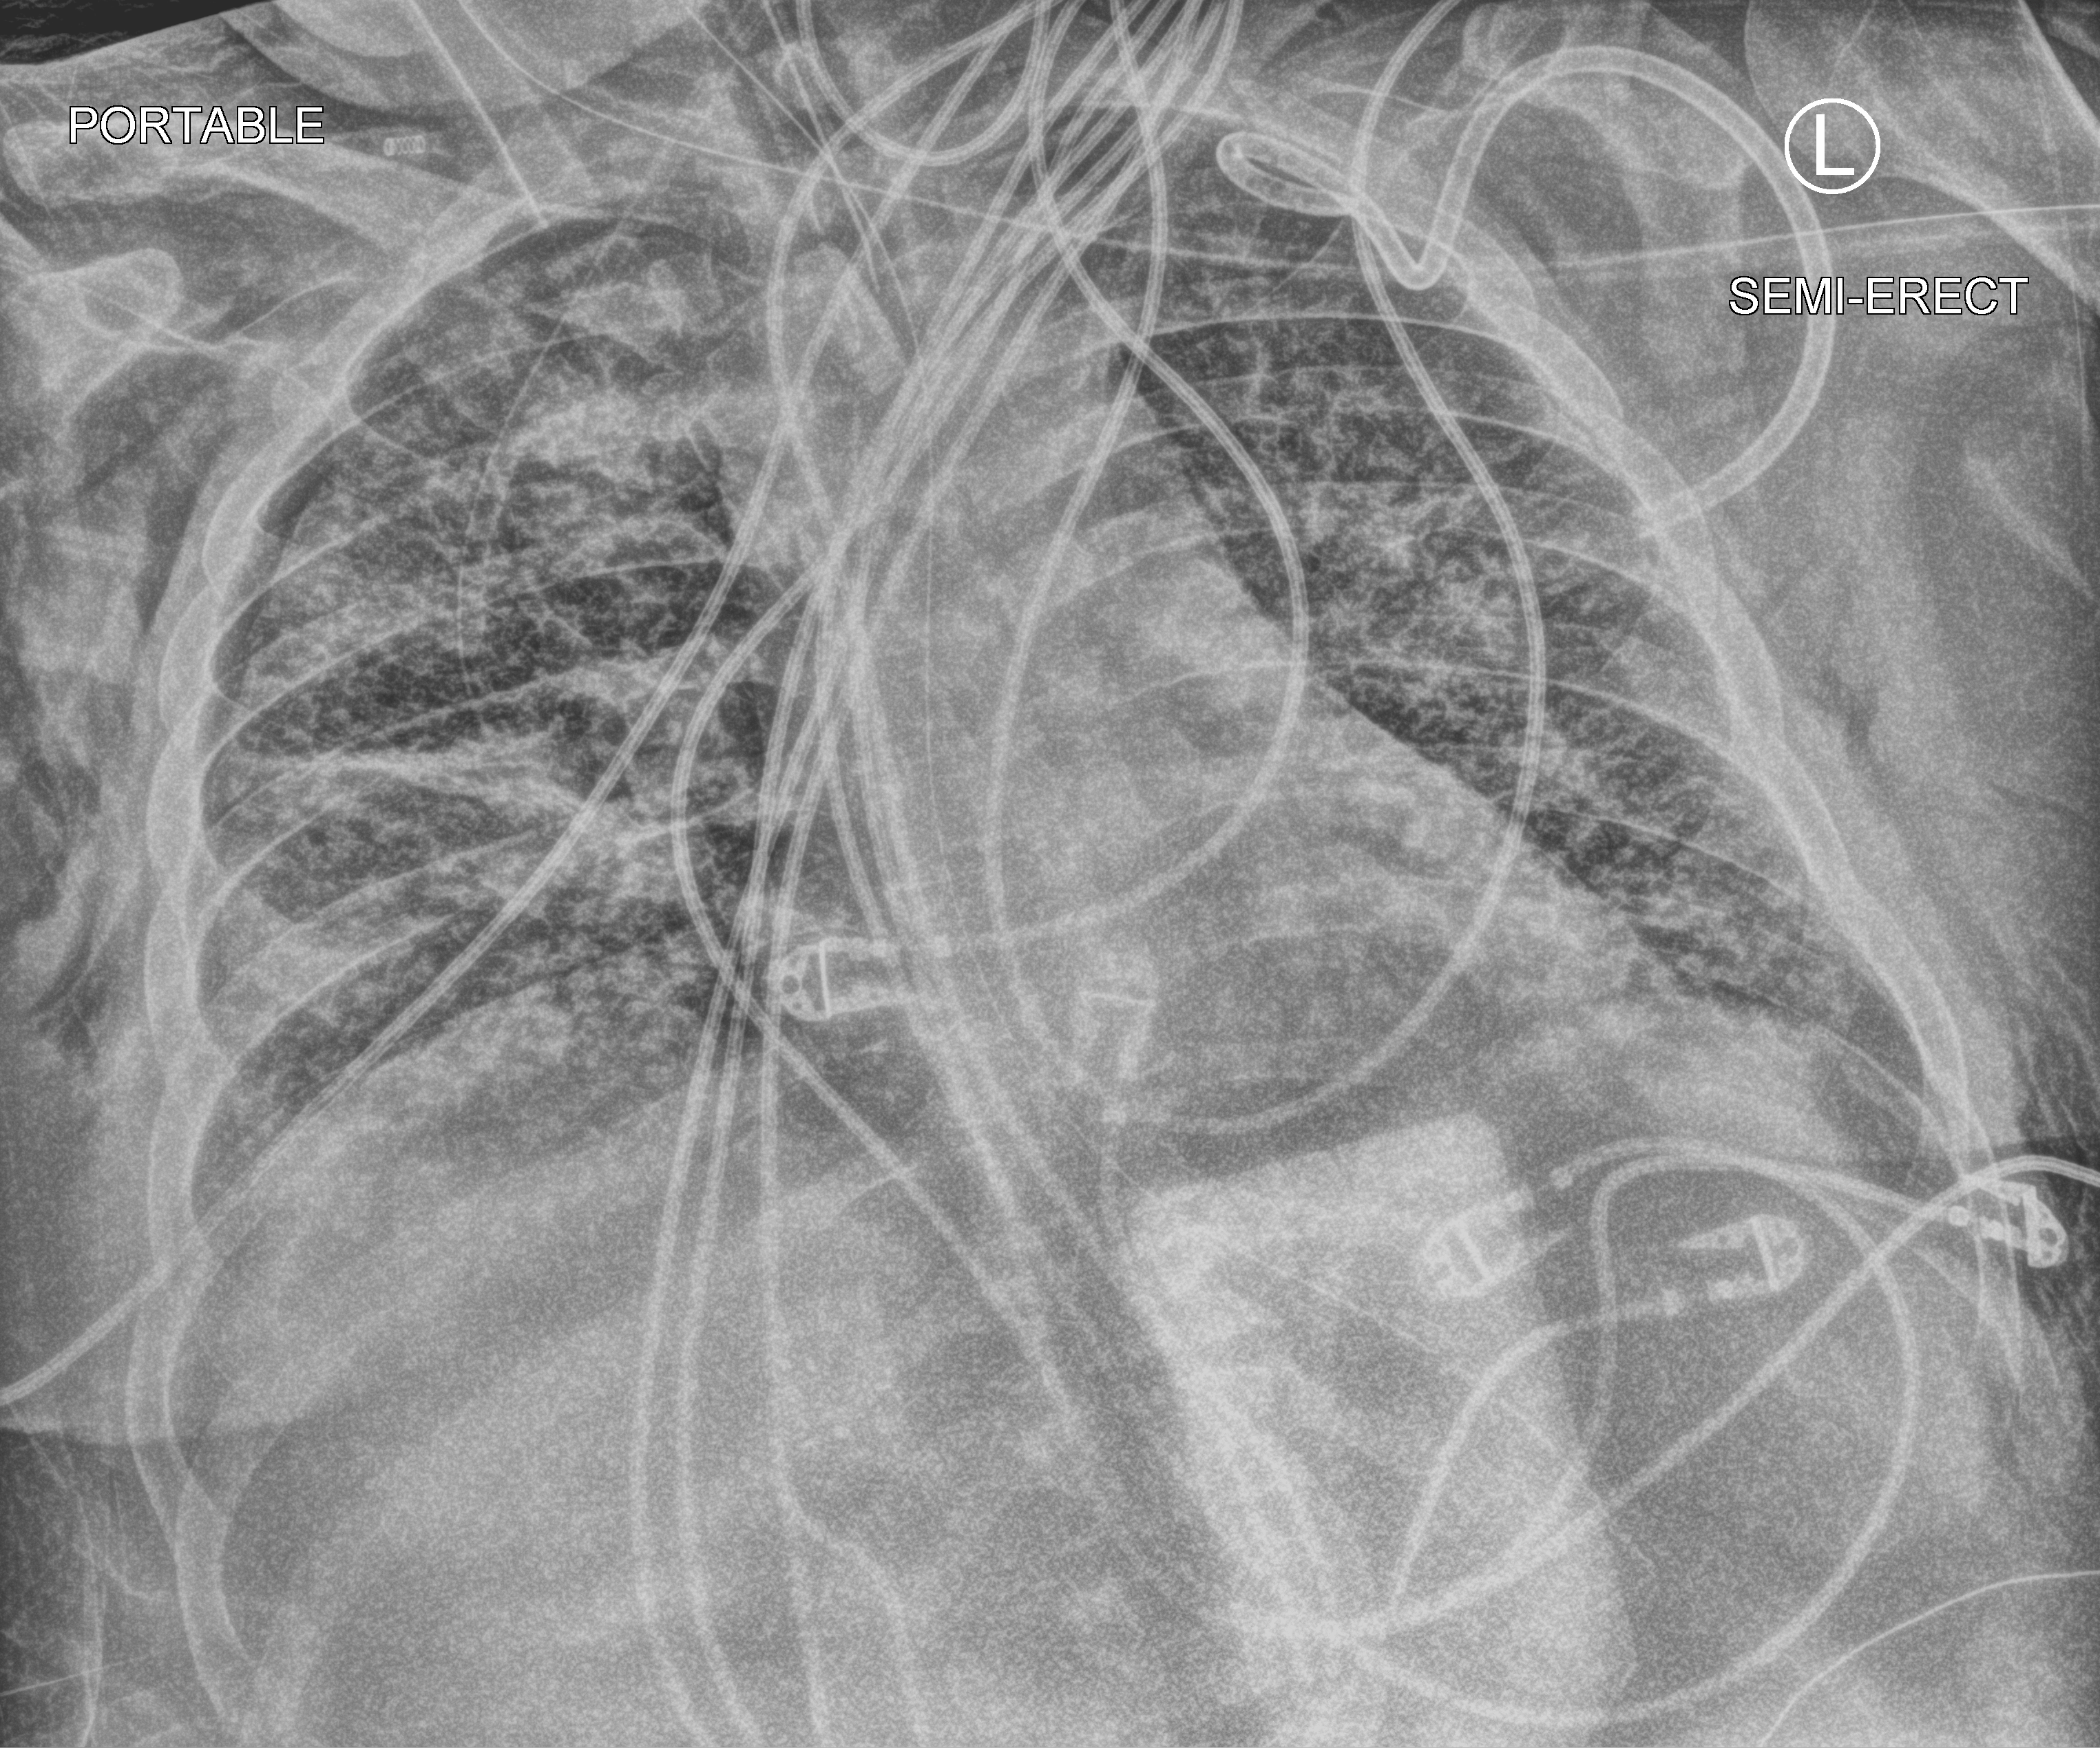
Bedside chest radiograph (computed radiography), anteroposterior (AP) projection. Adult patient hospitalised with COVID-19, age 18–59 years.
From the hospital-stay record, not from the radiograph (when in the stay this image was taken is not recorded): mechanically ventilated during this hospital stay: yes; admitted to intensive care during this hospital stay: yes.